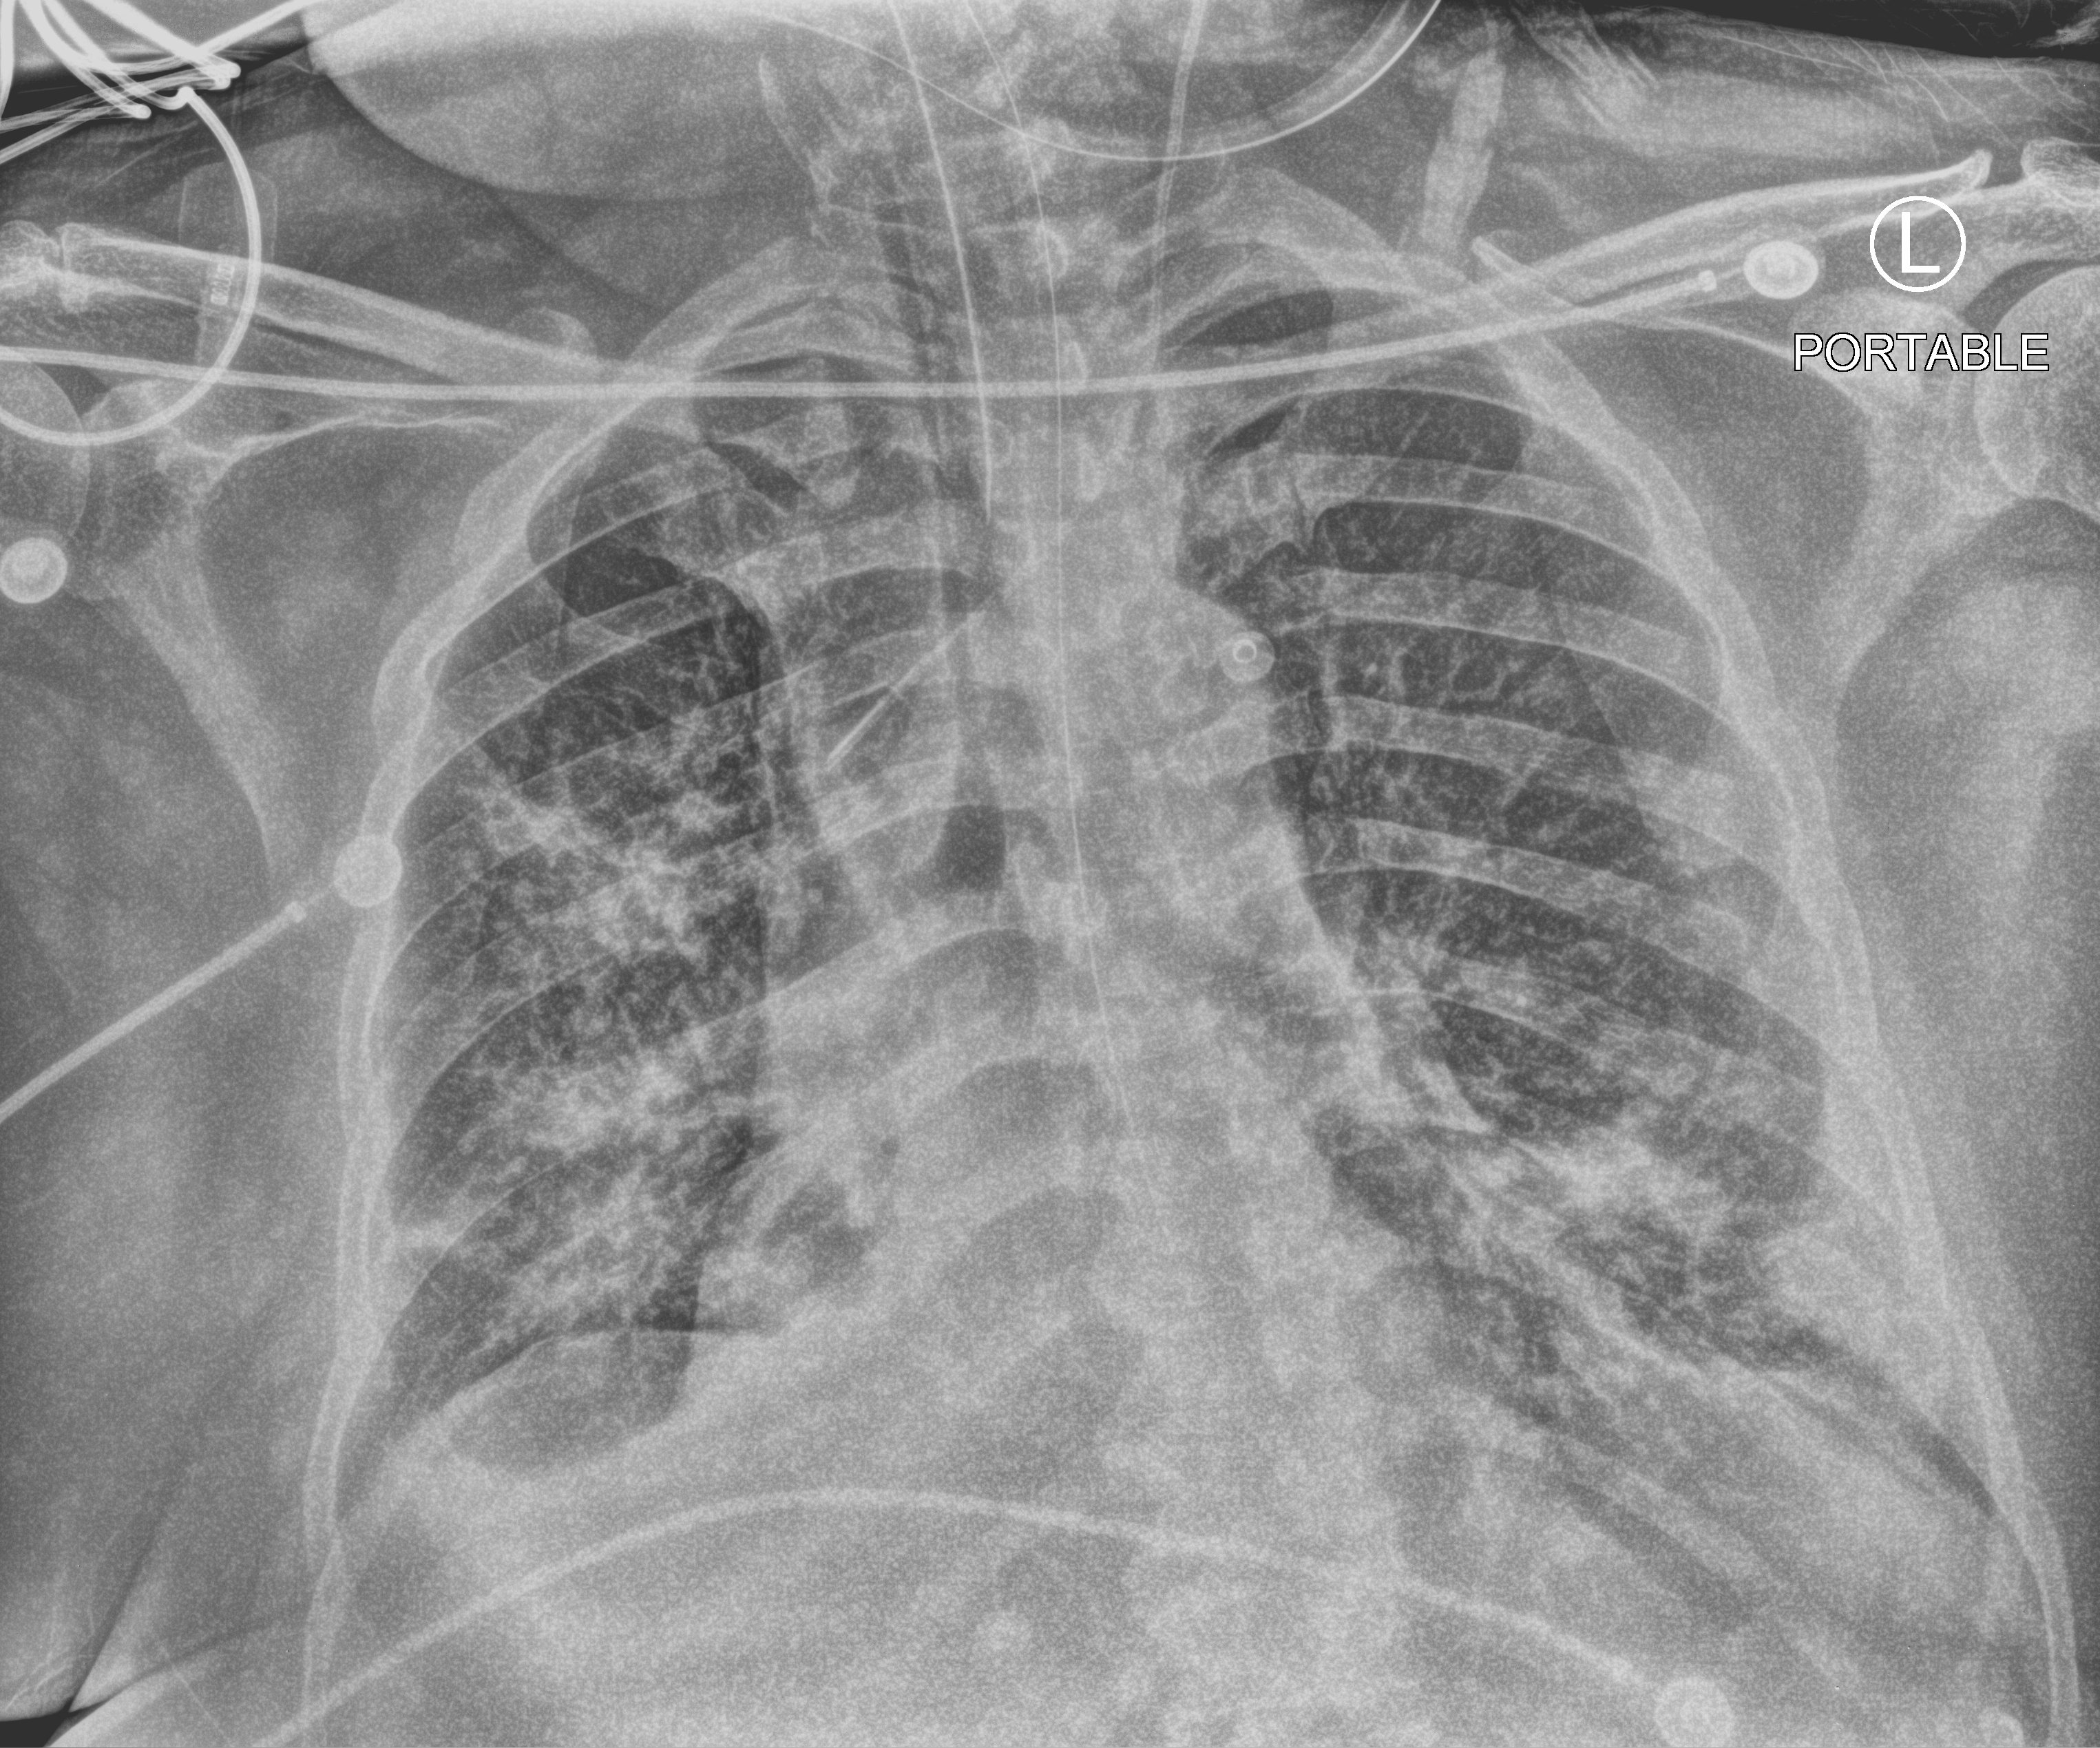
Portable chest radiograph, anteroposterior (AP) projection. Adult patient hospitalised with COVID-19, age 18–59 years.
Hospital-stay facts (about this admission, not read from this image; timing relative to this image not recorded): COPD (admission record): no; admitted to intensive care during this hospital stay: yes; hypertension (admission record): yes.